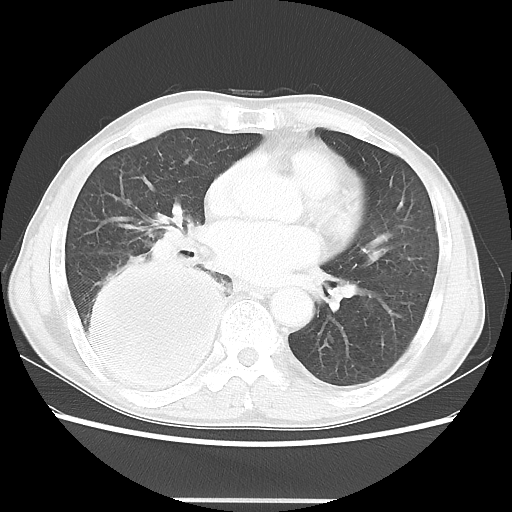
Chest CT, one axial slice; reconstruction kernel LUNG; lung window (W 1500 / L -600 HU); 5 mm slice thickness; 512 × 512 image matrix, field of view 361 × 361 mm. Patient: male, 66 years. From the clinical record (not read from this slice): clinical TNM (as recorded): T4 N1 M1; histopathological grade: G3.
Annotated regions visible in this slice (bounding box drawn by a radiologist):
- lung tumour (recorded histology: small cell carcinoma): bounding box (x1, y1, x2, y2) in pixels: (81, 249, 235, 415)